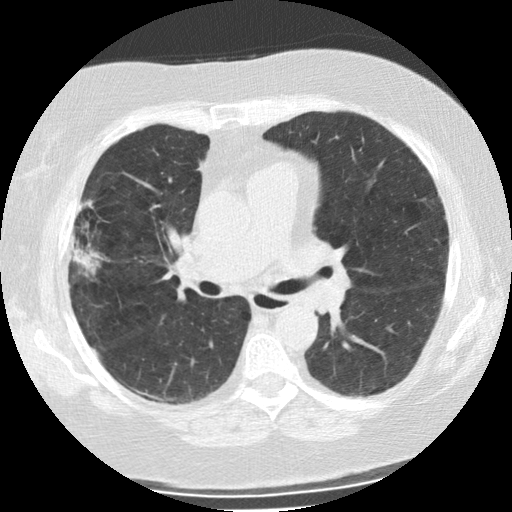
Low-dose screening chest CT, one axial slice; position 134 of 225 along the scan axis; reconstruction kernel STANDARD; lung window (W 1500 / L -600 HU); 512 × 512 image matrix.
Structures marked on this image (expert manual segmentation):
- lesion 1 (tumor, upper lobe of right lung): bounding box (x1, y1, x2, y2) in pixels: (73, 225, 103, 275)